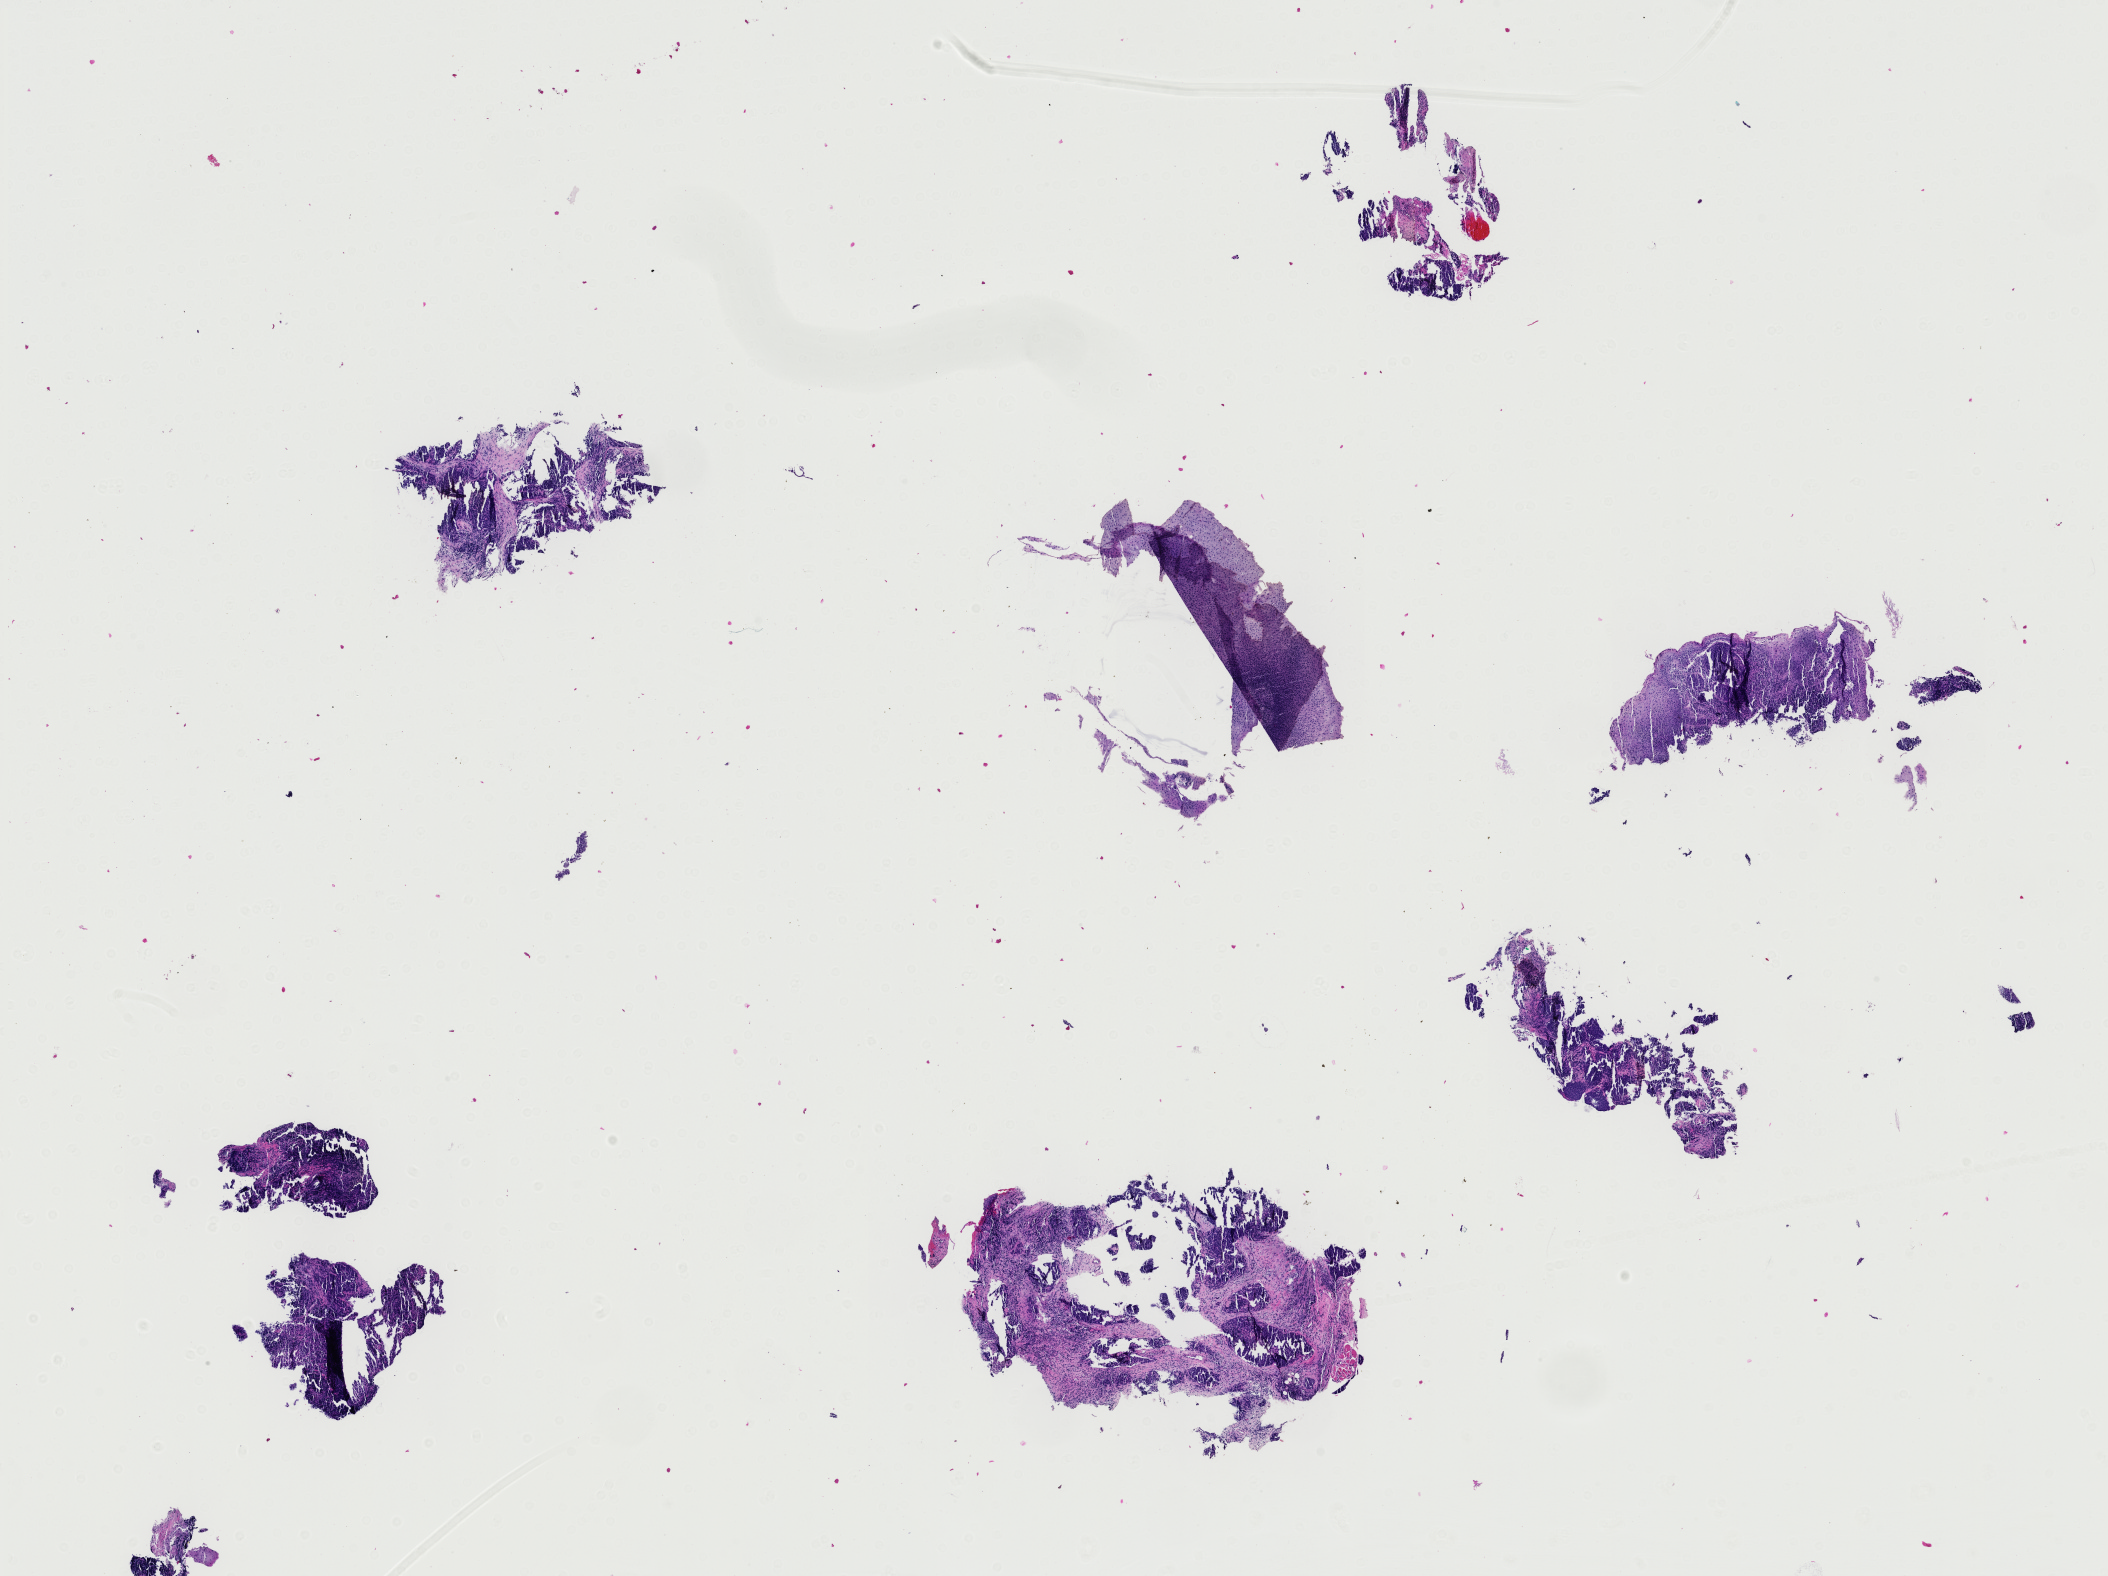
Whole-slide histology image, H&E-stained — shown as a low-resolution overview of the whole scanned area (about 15.3 x 11.4 mm). Formalin-fixed paraffin-embedded (FFPE) diagnostic section. Sample: primary tumour, head and neck. Patient: male, age at initial diagnosis 61 years. Histologic grade: GX (grade cannot be assessed).
Pathologic diagnosis: Squamous cell carcinoma, large cell, nonkeratinizing, NOS (tonsil, NOS).